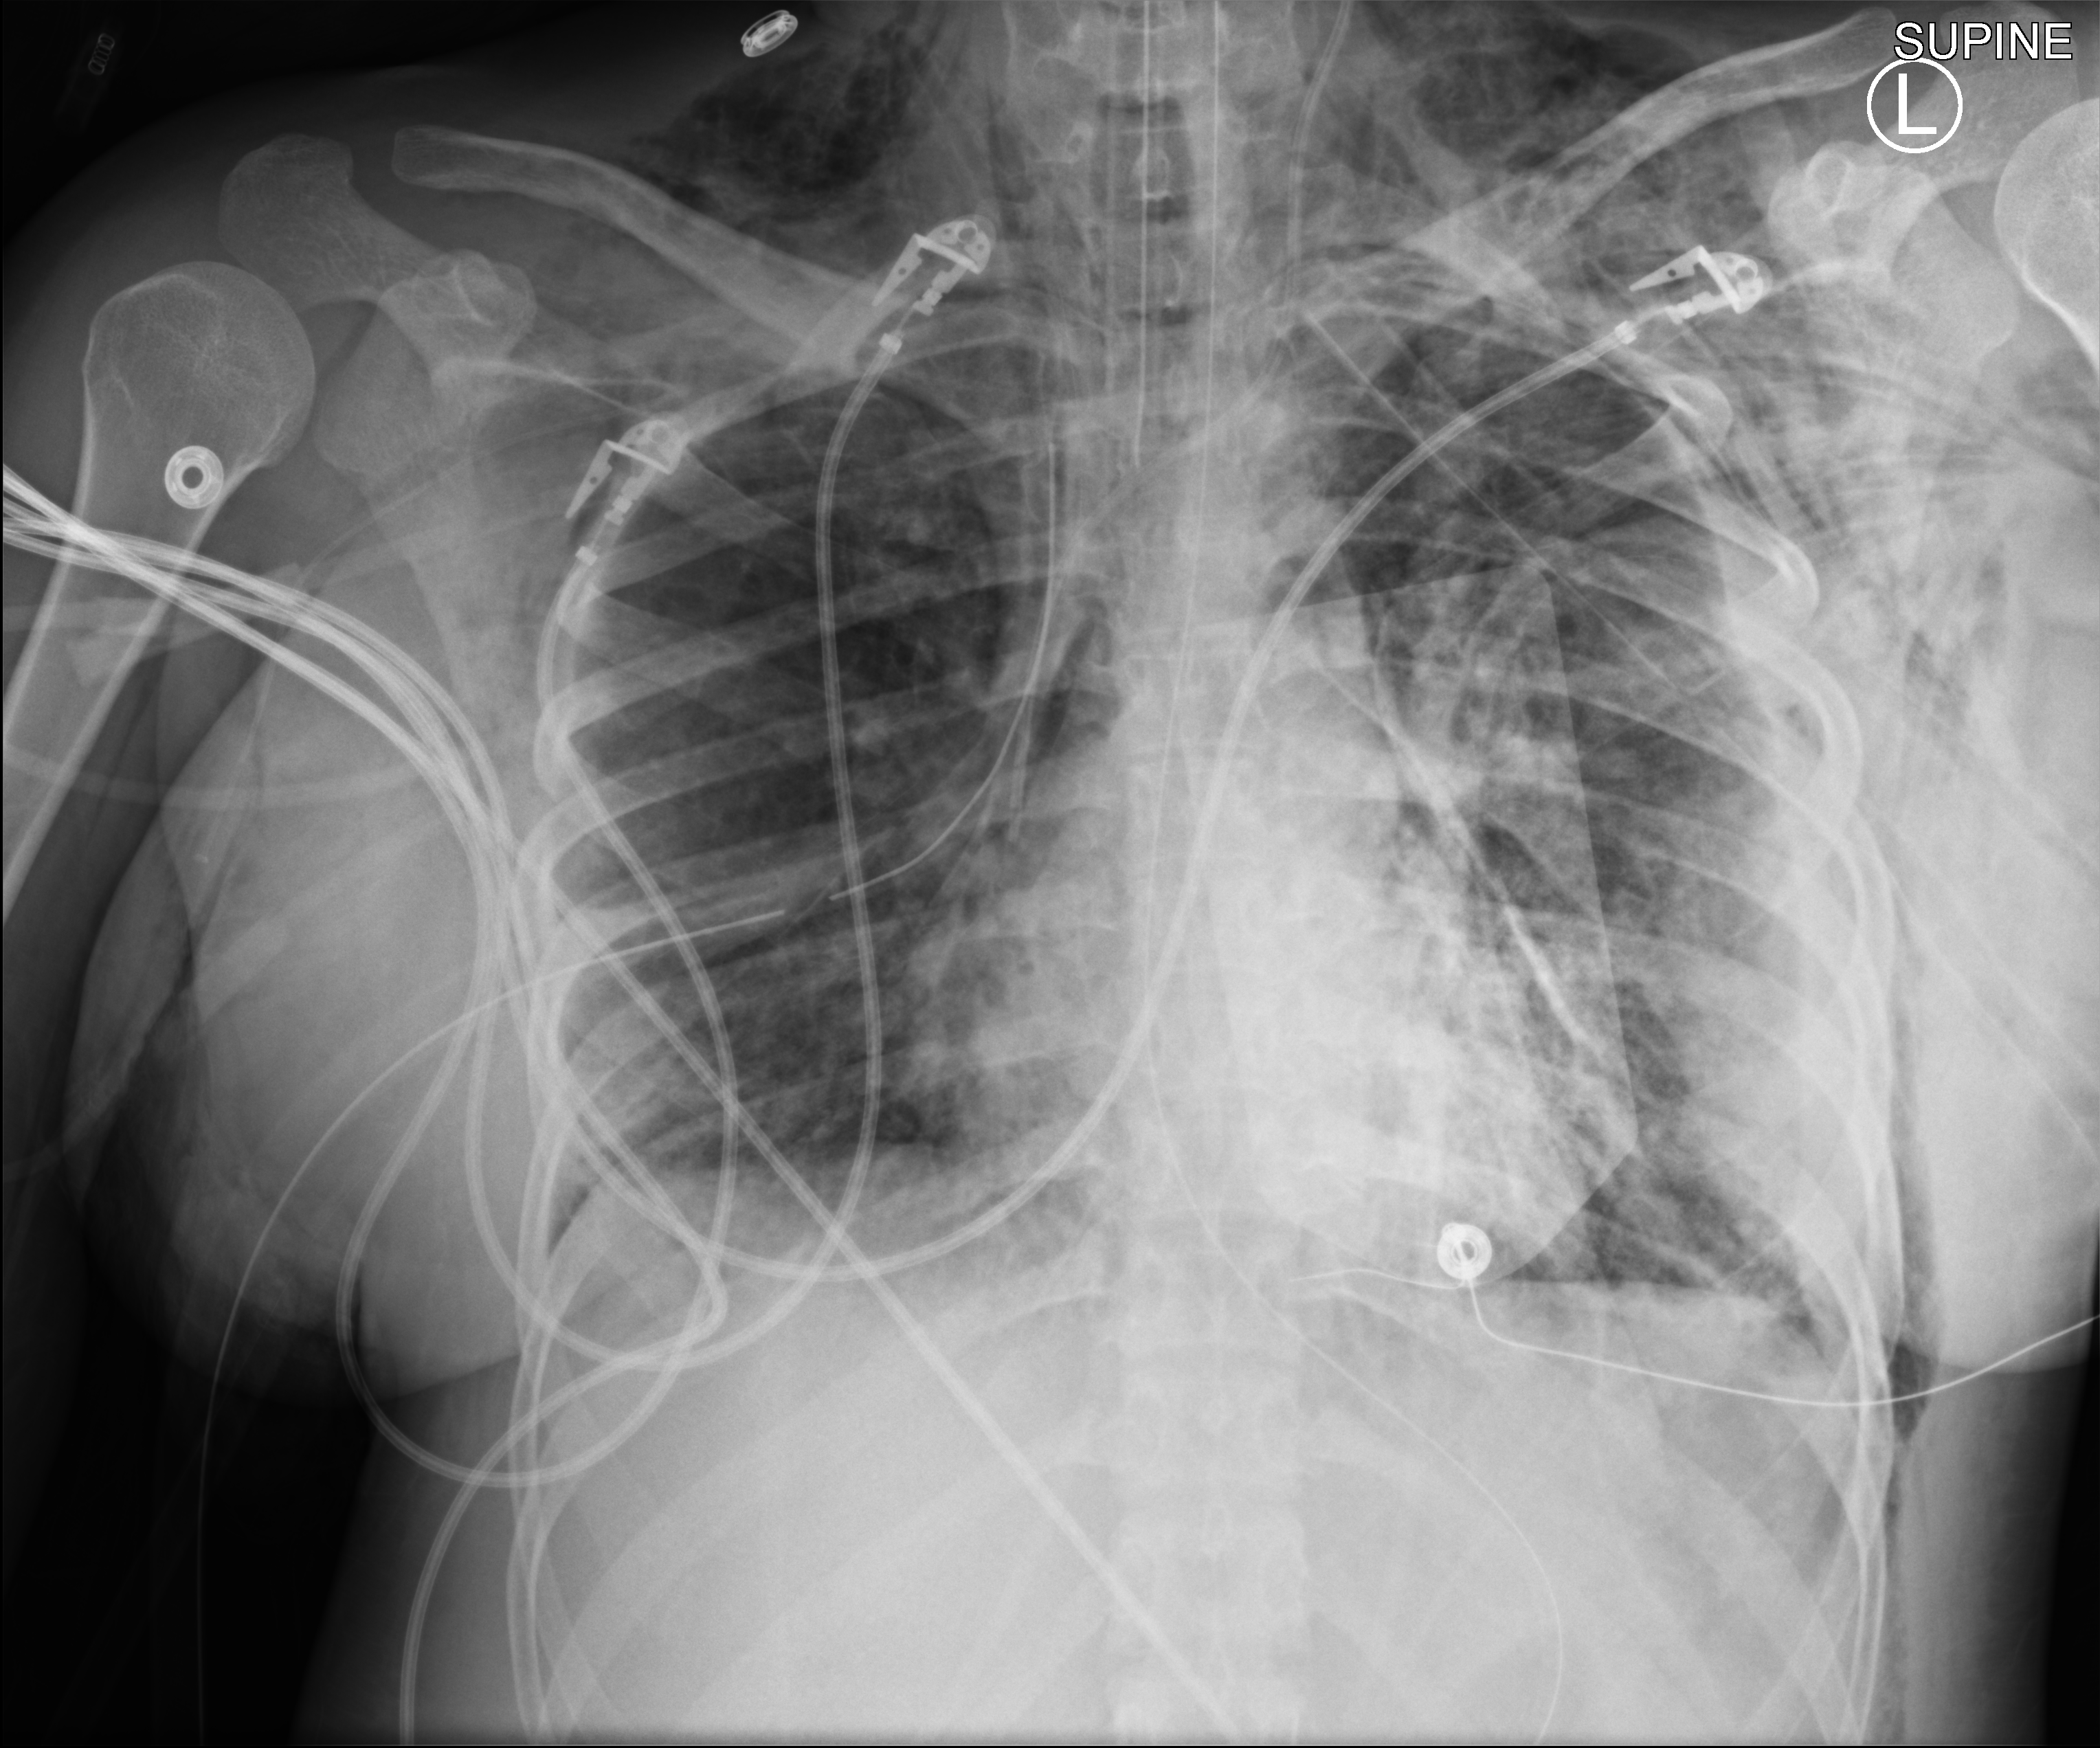
Chest X-ray (portable); anteroposterior (AP) projection. Patient hospitalised with COVID-19, aged 18–59 years.
Hospital-stay facts (about this admission, not read from this image; timing relative to this image not recorded): smoking status (admission record): never.